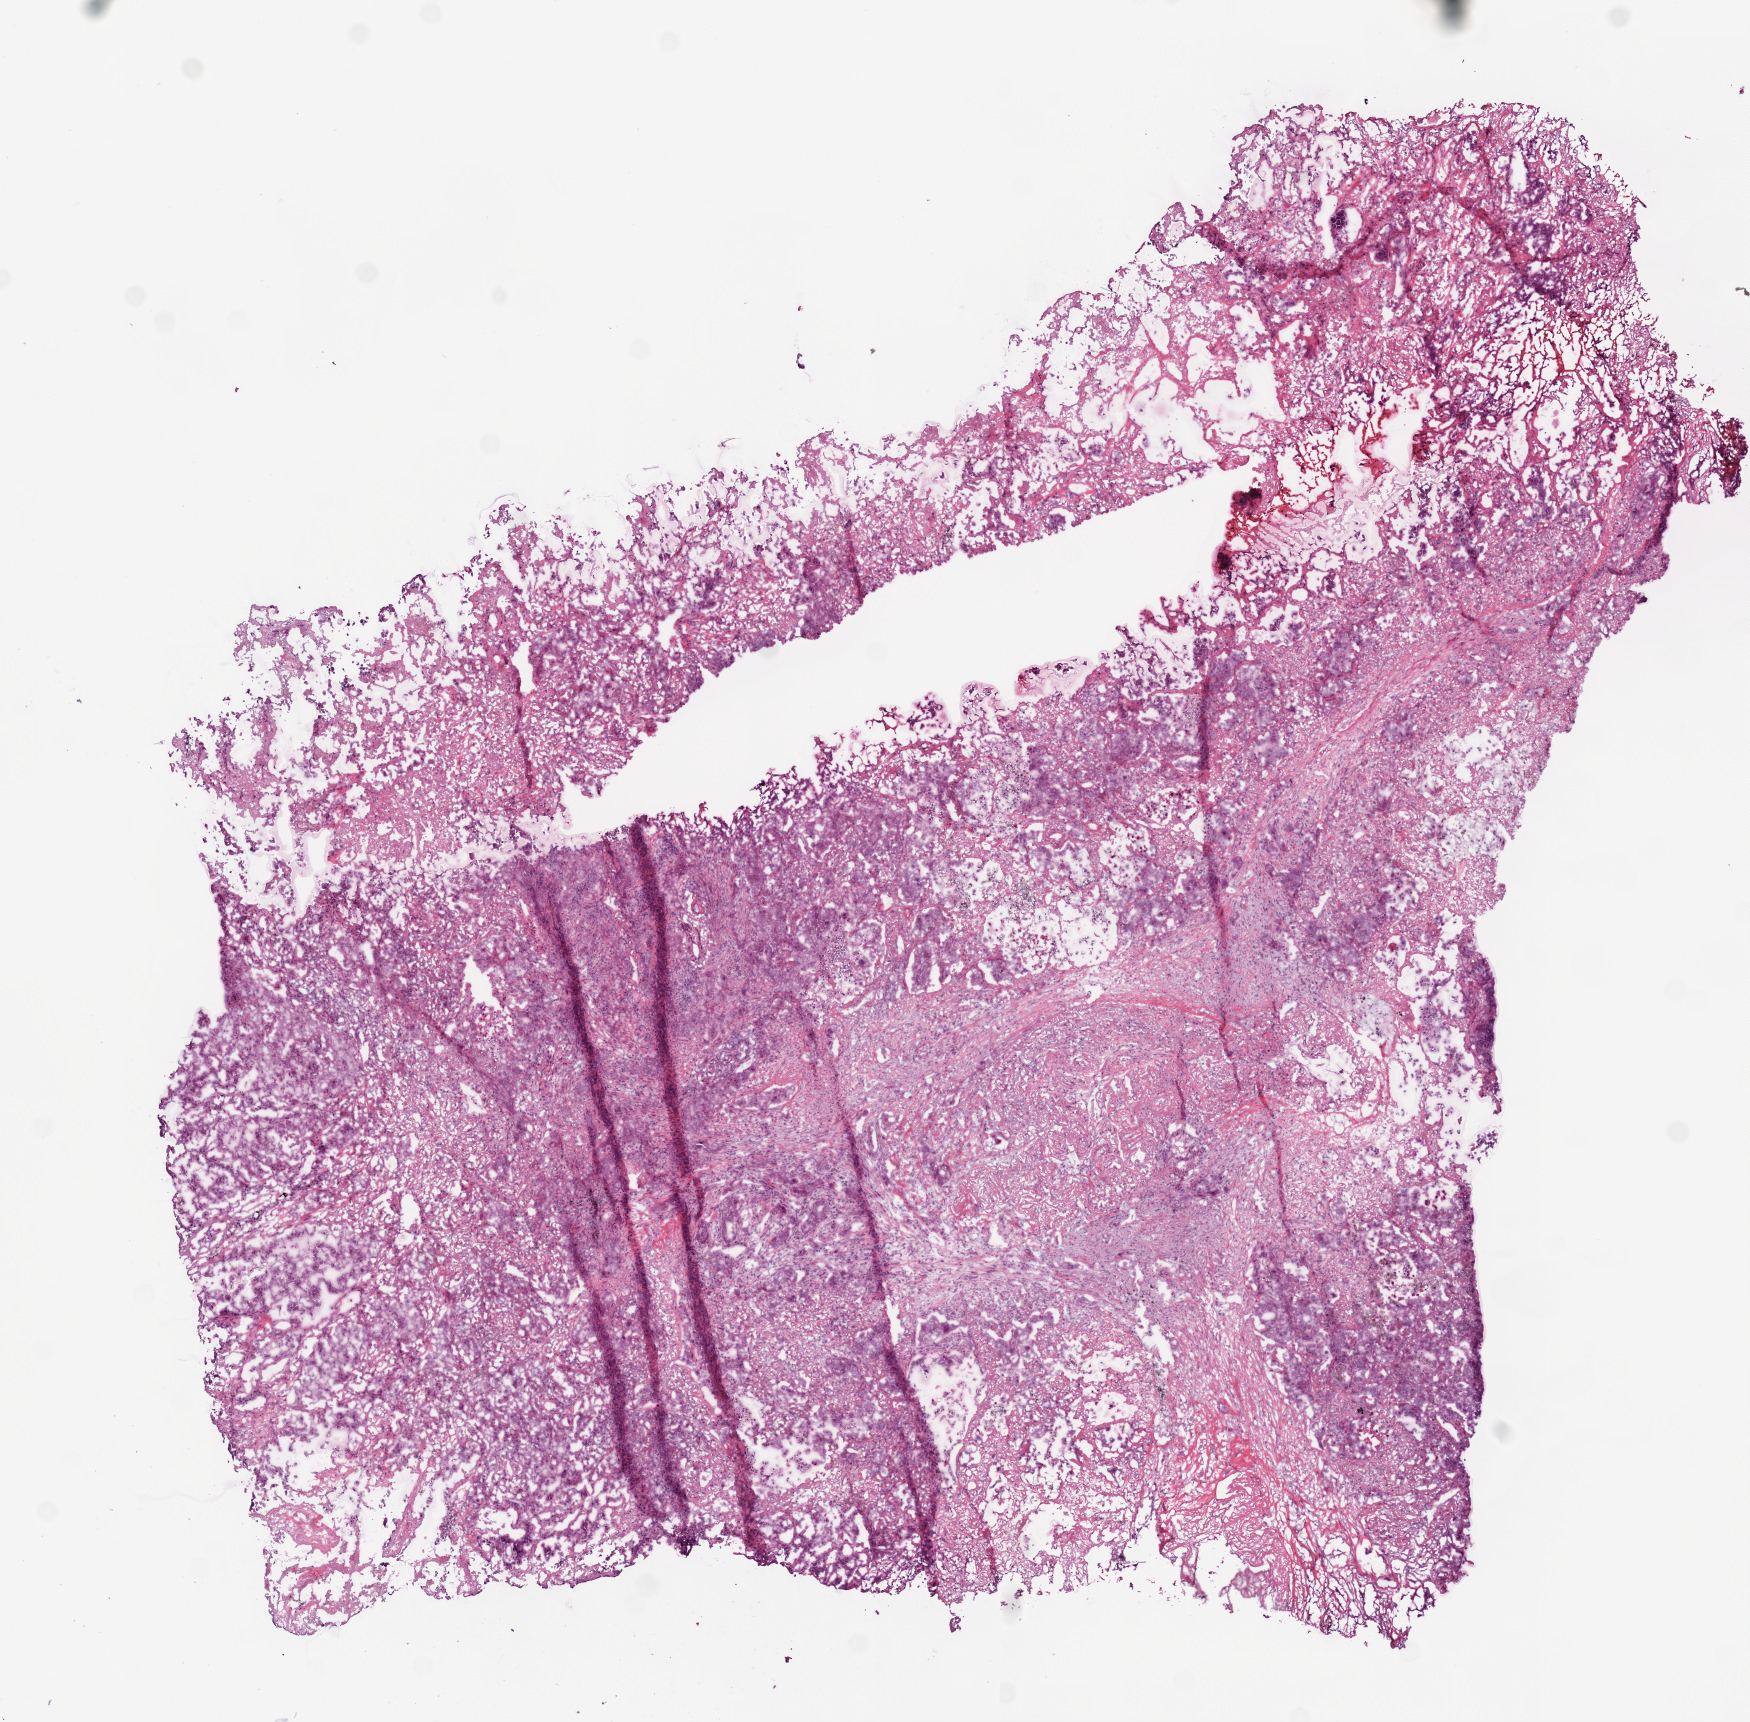
Digitized H&E tissue section (whole slide) — shown as a low-resolution overview of the whole scanned area (about 7.0 x 6.9 mm); frozen section; sample: primary tumour, lung. Female, age 58 years at initial diagnosis. Composition of this section per pathologist review: tumour cells 20%, tumour nuclei 55%, normal cells 0%, stromal cells 45%, necrosis 35%.
• laterality: right
• histologic diagnosis: Adenocarcinoma, NOS (upper lobe, lung)
• AJCC pathologic stage: IIIA (6th edition)